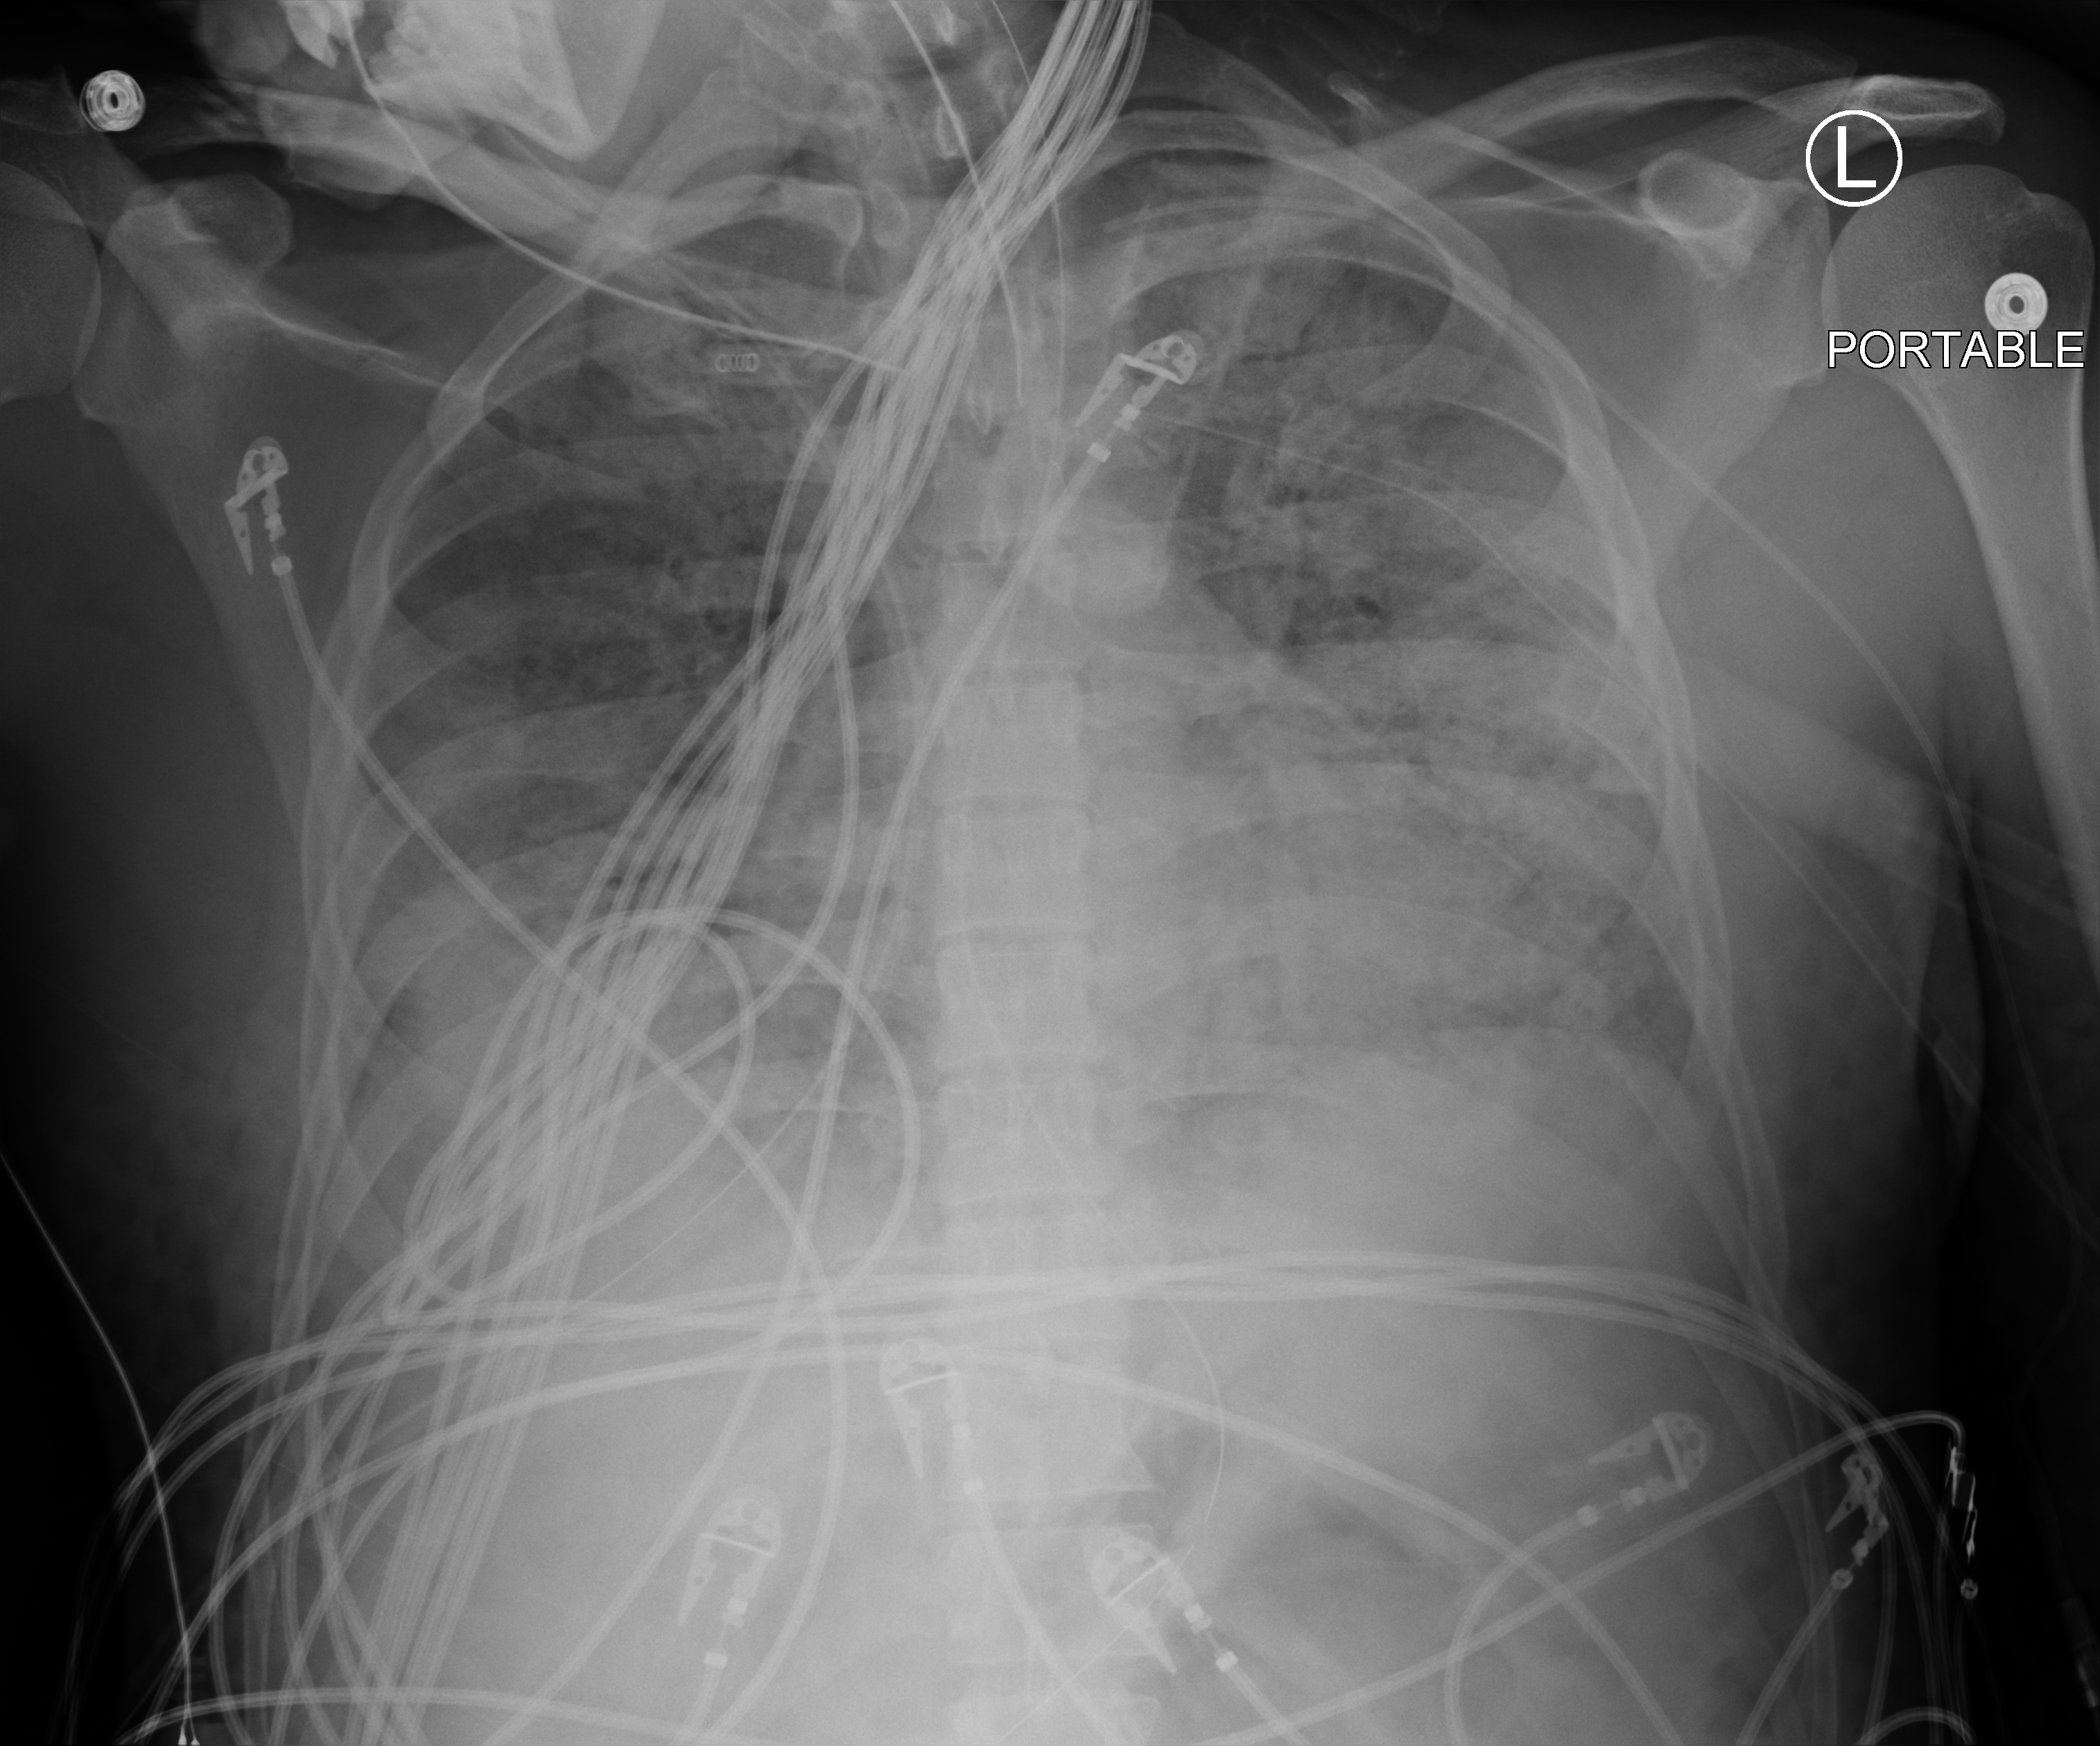
Portable chest radiograph; anteroposterior (AP) projection. Male patient hospitalised with COVID-19, age 18–59 years.
Admission-level facts for this patient (not findings on this image; timing relative to this image not recorded): COPD (admission record): no; admitted to intensive care during this hospital stay: yes.